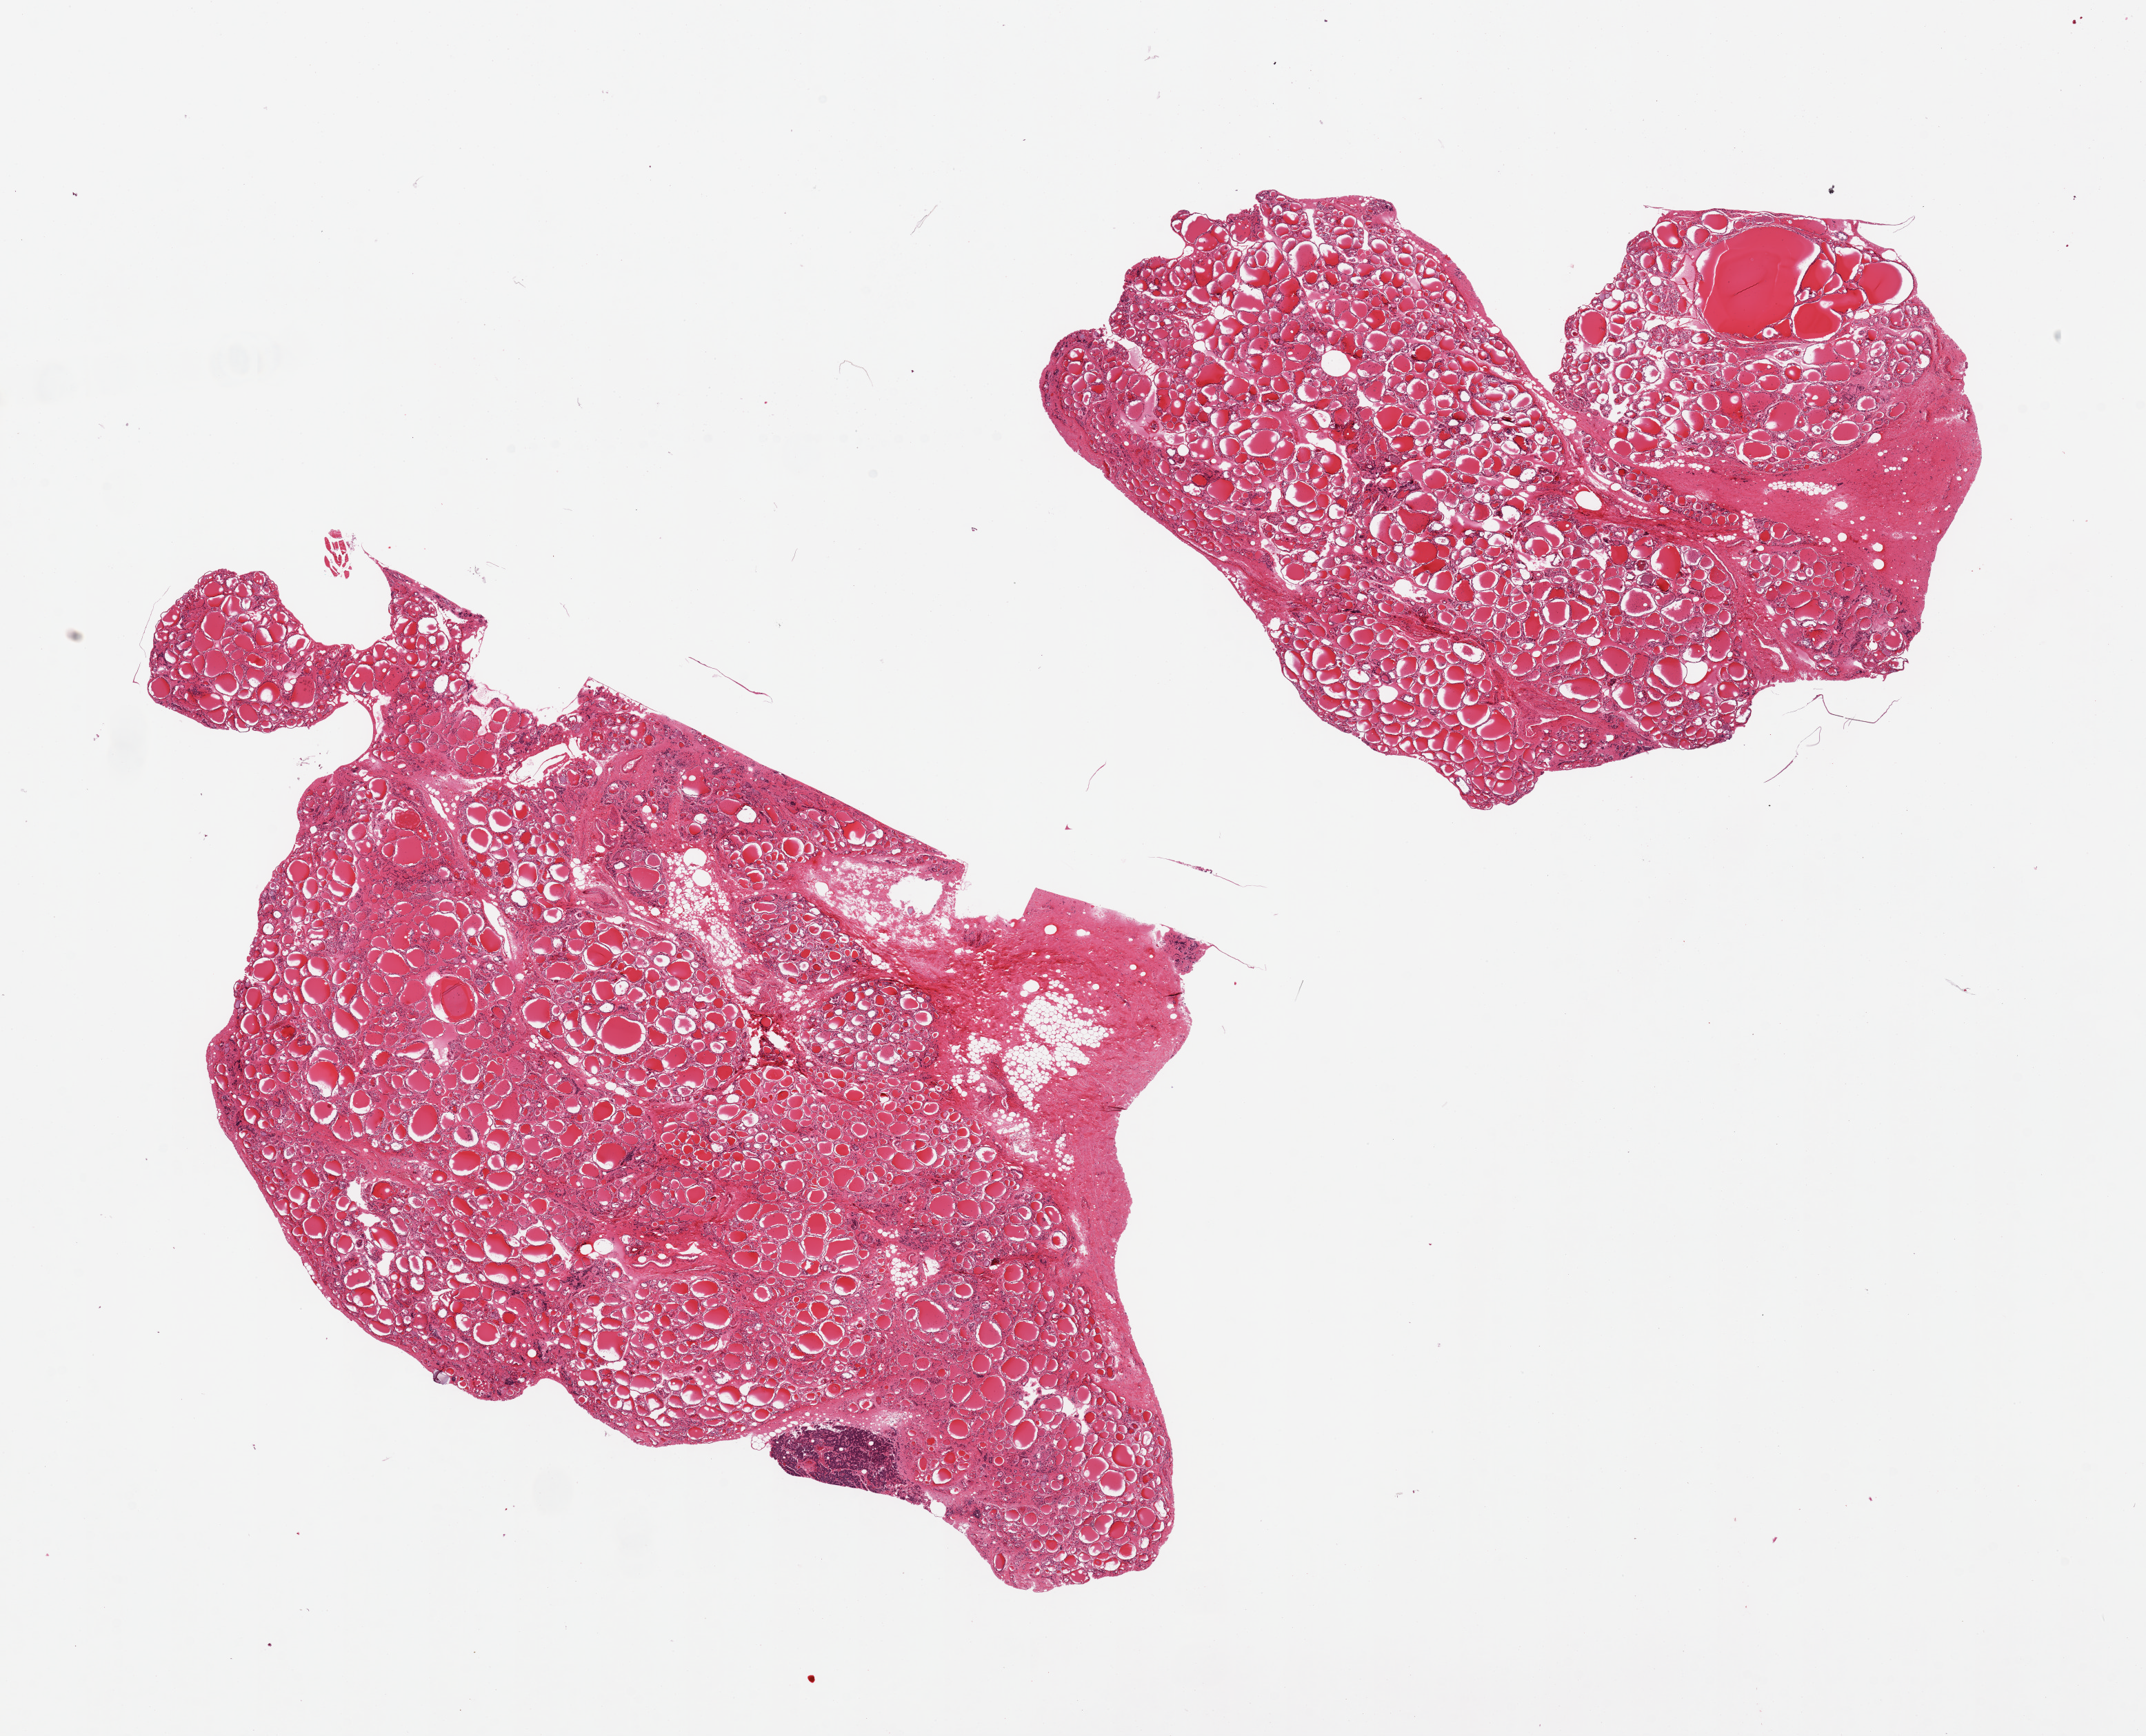
Whole-slide image, haematoxylin and eosin stain — shown as a low-resolution overview of the whole scanned area (about 24.6 x 19.9 mm, acquisition: 20x scan); PAXgene-fixed, paraffin-embedded tissue; sampled site (target tissue): thyroid; donor tissue sample. Donor sex: female.
Reviewer comment on this tissue sample: 2 pieces, incidental 1.5mm parathyroid fragment, prominent regressive changes, features of mulitnodular goiter in thyroid; Adherent fat/fibrous tissue nubbins up to ~2.5mm.